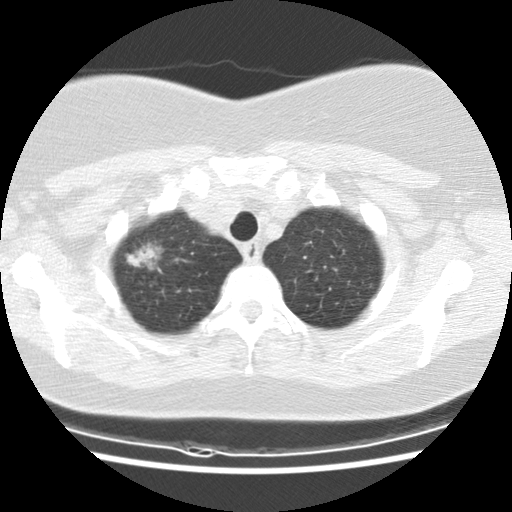
Low-dose screening chest CT, one axial slice; slice 117 of 132 in the series (ordered by position); 120 kVp; lung window (W 1500 / L -600 HU); 2.5 mm slice thickness; 512 × 512 image matrix, field of view 326 × 326 mm.
Structures marked on this image (expert manual segmentation):
- lesion 1 (tumor, upper lobe of right lung): bounding box [x1, y1, x2, y2] px = [126, 241, 162, 273]